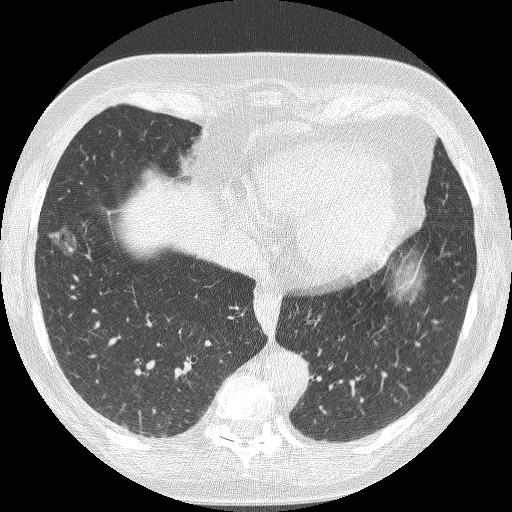
Chest CT (low-dose screening protocol), one axial image. Baseline screening round. Lung window (W 1500 / L -600 HU). 1.25 mm slice thickness. Lung (sharp) reconstruction kernel (BONE). Slice 71 of 221 in the series. 512 × 512 image matrix. Female participant, aged 68 years at enrolment. Current smoker at enrolment.
Expert-annotated lung lesion, bounding box (x1, y1, x2, y2) in pixels: (33, 224, 85, 276). Reader record for this screening exam (exam-level; its link to the box is not recorded): non-calcified nodule or mass ≥4 mm, right lower lobe, 16 × 12 mm, poorly defined margins, ground glass attenuation. Later outcome: lung cancer diagnosed 406 days after this screen — bronchiolo-alveolar adenocarcinoma, NOS, right lower lobe, well differentiated (G1), stage IA (AJCC 6th edition), 13 mm at pathology.